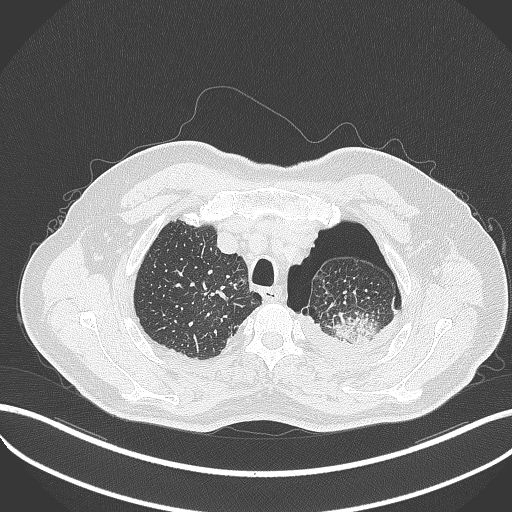
Chest CT, one axial slice. Slice 419 of 464 in the series (ordered by position). Reconstruction kernel B70f. Lung window (W 1500 / L -600 HU). 512 × 512 image matrix. Patient: male, 76 years. From the clinical record (not read from this slice): clinical TNM (as recorded): T3 N0 M1b.
Annotated regions visible in this slice (bounding box drawn by a radiologist):
- lung tumour (recorded histology: adenocarcinoma): bounding box <329,310,382,345> (left, top, right, bottom; pixels)